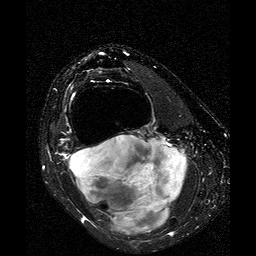
MRI of an extremity soft-tissue mass, one axial slice. Slice 18 of 25 in the series (ordered by position). T2-weighted fat-saturated. 256 × 256 image matrix. Female patient. From the clinical record (not read from this slice): histological type: liposarcoma; site of the primary tumour: right thigh.
Outlined on this slice (outlined manually by an expert reader):
- gross tumour volume (mass): bounding box <68,135,187,236> (left, top, right, bottom; pixels)